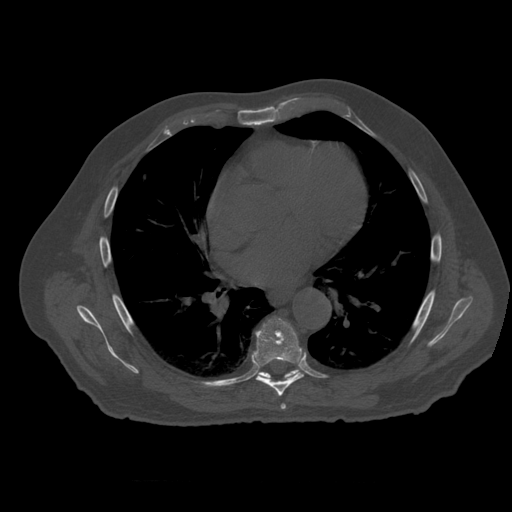
CT including the spine, one axial slice; slice 356 of 399 in the series (ordered by position); reconstruction kernel STANDARD; bone window (W 1800 / L 400 HU); 1.25 mm slice thickness; 512 × 512 image matrix, field of view 407 × 407 mm. Patient age 73 years. Case-level facts recorded for this patient, not image findings: primary cancer: prostate; vertebrae with lytic lesions (as recorded): L2.
Structures marked on this image (semi-automatic segmentation, software-assisted and operator-edited):
- T6 vertebra: bounding box [x1, y1, x2, y2] px = [281, 404, 287, 410]
- T7 vertebra: [252, 318, 304, 397]
- T8 vertebra: [259, 370, 299, 379]